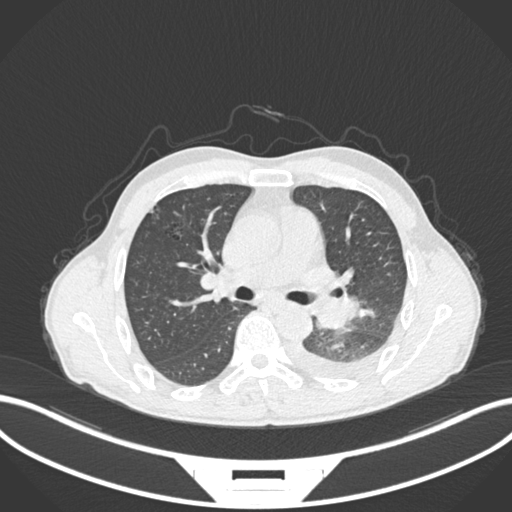
Chest CT, one axial slice. Position 150 of 222 along the scan axis. Reconstruction kernel B30f. 120 kVp. Lung window (W 1500 / L -600 HU). 1 mm slice thickness. 512 × 512 image matrix, field of view 400 × 400 mm. Patient: male, 47 years. Case-level facts recorded for this patient, not image findings: clinical TNM (as recorded): T3 N1 M1c.
Outlined on this slice (bounding box drawn by a radiologist):
- lung tumour (recorded histology: small cell carcinoma): box from (x=306, y=293) to (x=361, y=329) px